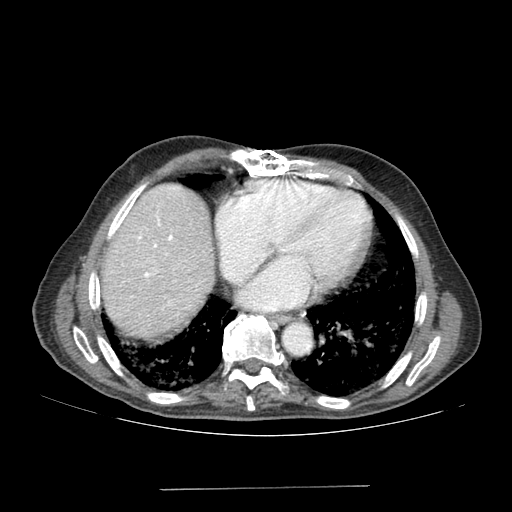
Contrast-enhanced abdominal CT (liver protocol), one axial slice. Position 164 of 192 along the scan axis. 120 kVp. Soft-tissue window (W 400 / L 40 HU). 2.5 mm slice thickness. 512 × 512 image matrix, field of view 400 × 400 mm. From the clinical record (not read from this slice): diagnosis: hepatocellular carcinoma (patient treated with transarterial chemoembolisation; whether this scan precedes or follows treatment is not stated here); TNM stage (as recorded): Stage-IVA; Child-Pugh class: A; tumour differentiation: poorly differentiated; tumour nodularity: uninodular.
Structures marked on this image (semi-automatically segmented with operator editing):
- liver parenchyma outside the tumour (the mass and vessels are separate outlines, so this box may not span the whole liver): box from (x=102, y=184) to (x=214, y=336) px
- liver vessels: (x=138, y=217)–(x=173, y=277)